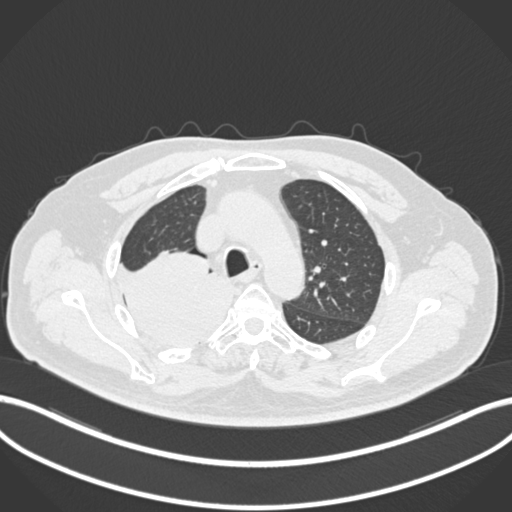
Chest CT, one axial slice. Position 153 of 218 along the scan axis. Reconstruction kernel B30f. 120 kVp. Lung window (W 1500 / L -600 HU). 1 mm slice thickness. 512 × 512 image matrix, field of view 400 × 400 mm. Male patient, age 68 years. Case-level facts recorded for this patient, not image findings: clinical TNM (as recorded): T2a N0 M0.
Structures marked on this image (bounding box drawn by a radiologist):
- lung tumour (recorded histology: adenocarcinoma): box from (x=115, y=251) to (x=233, y=347) px